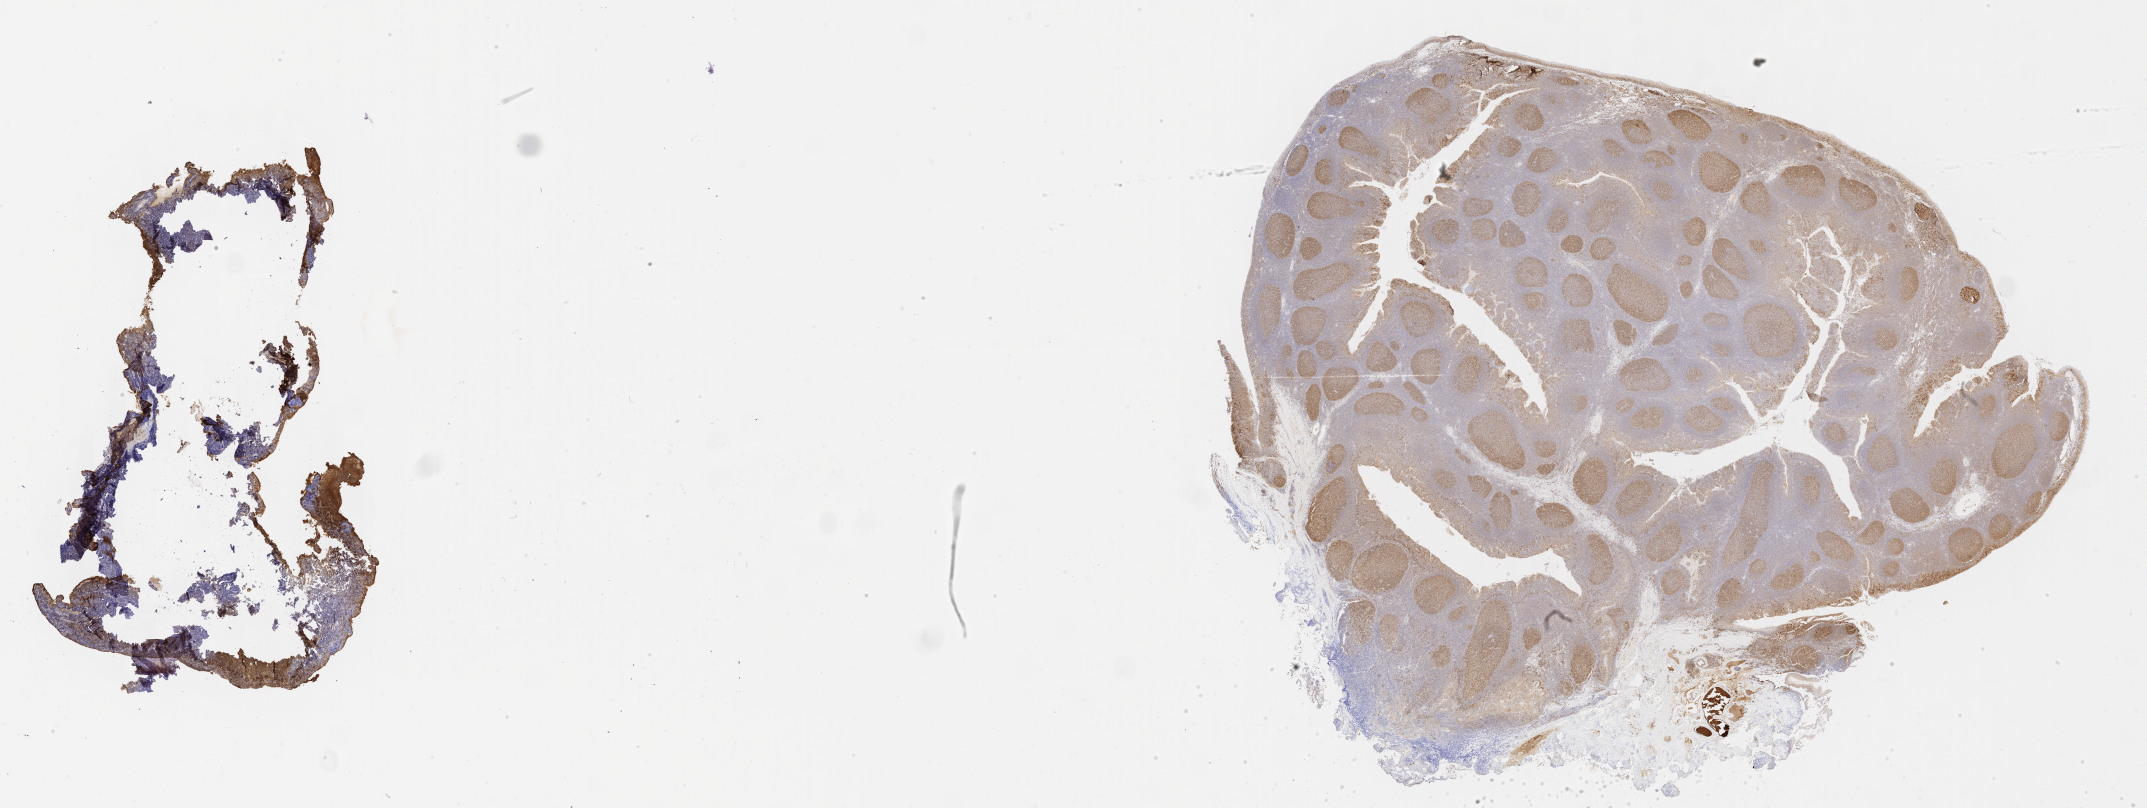
Immunohistochemistry (IHC) whole-slide image stained for BCL6, shown as a low-resolution overview of the whole scanned area (about 34.7 x 13.1 mm). Specimen: tumor tissue. Anatomic site: cranium. Patient female; age 10 years.
Histologic diagnosis: Burkitt lymphoma, NOS.